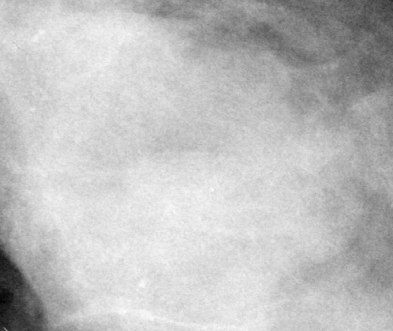
Region of interest cut from a scanned film mammogram (one marked finding), left breast, CC view, BI-RADS breast density category 4 (scale 1–4).
- Marked abnormality: mass, shape oval, margins obscured; BI-RADS assessment category 3; pathology result (as recorded, not read from the image): benign.